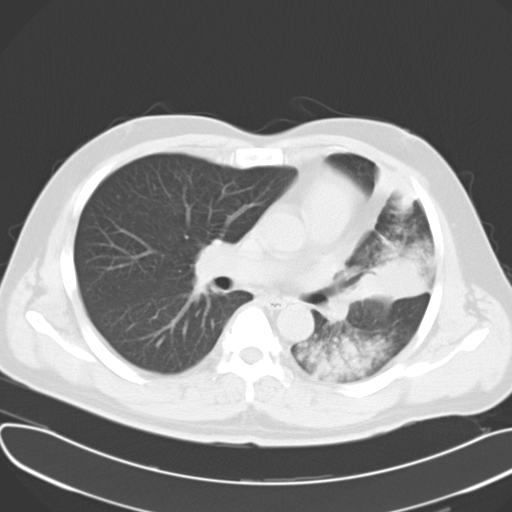
Chest CT, one axial slice; slice 18 of 30 in the series (ordered by position); reconstruction kernel B40f; 120 kVp; lung window (W 1500 / L -600 HU); 10 mm slice thickness; 512 × 512 image matrix, field of view 377 × 377 mm. Male patient, age 48 years. From the clinical record (not read from this slice): clinical TNM (as recorded): T4 N0 M0.
Outlined on this slice (bounding box drawn by a radiologist):
- lung tumour (recorded histology: adenocarcinoma): bounding box [x1, y1, x2, y2] px = [337, 257, 428, 307]